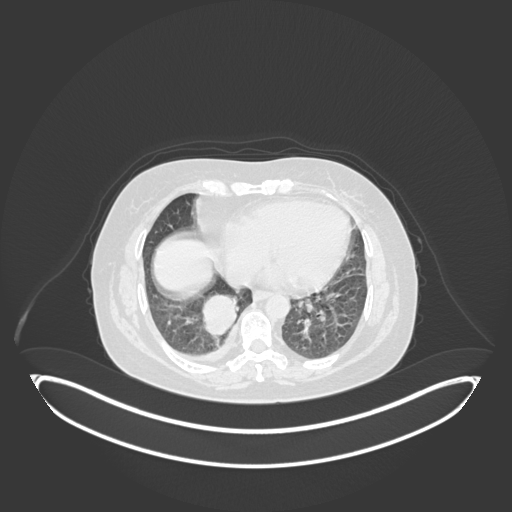
Chest CT, one axial slice. Position 49 of 231 along the scan axis. Reconstruction kernel B30f. 120 kVp. Lung window (W 1500 / L -600 HU). 1 mm slice thickness. 512 × 512 image matrix. Female patient, age 56 years. From the clinical record (not read from this slice): clinical TNM (as recorded): T2b N1 M0; histopathological grade: G3.
Annotated regions visible in this slice (rectangle marked by the reading radiologist):
- lung tumour (recorded histology: small cell carcinoma): bounding box (x1, y1, x2, y2) in pixels: (201, 291, 248, 341)